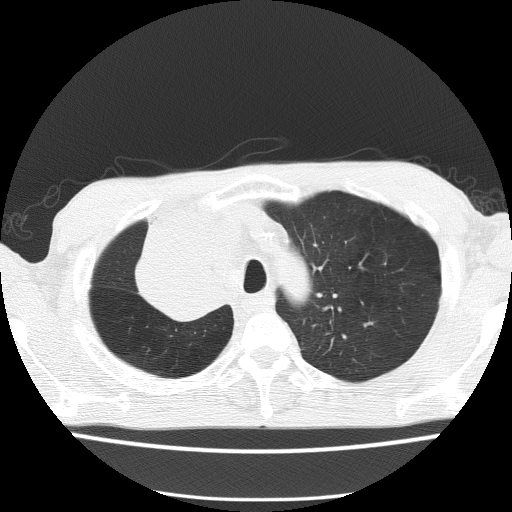
Axial slice from a low-dose chest CT screening exam; baseline annual screen; lung window (W 1500 / L -600 HU); 120 kVp; 512 × 512 image matrix. Male, age 59 years at enrolment. Former smoker at enrolment.
Expert-annotated lung lesion, bounding box [x1, y1, x2, y2] px = [129, 235, 240, 327]. The screening reader recorded 5 non-calcified nodules or masses ≥4 mm on this exam (left upper lobe, left upper lobe, left upper lobe, right middle lobe, right lower lobe); which of them this box marks is not recorded. Official screen result: positive, change unspecified: nodule(s) >= 4 mm or enlarging nodule(s), mass(es), or other non-specific abnormalities suspicious for lung cancer. Later outcome: lung cancer diagnosed 72 days after this screen — squamous cell carcinoma, NOS, right upper lobe, moderately differentiated (G2), stage IV (AJCC 6th edition).